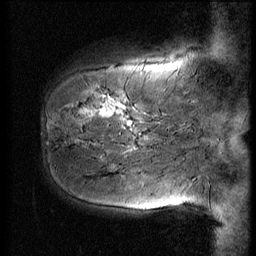
Breast MRI (dynamic contrast-enhanced), one sagittal slice. 3 images stored at this slice position (order not interpretable as contrast timing). 1.5 T. TE 4.2 ms, TR 9 ms. 2.5 mm slice thickness. 256 × 256 image matrix, field of view 180 × 180 mm. Female patient, age 51 years. Case-level facts recorded for this patient, not image findings: setting: breast cancer imaged before/during neoadjuvant chemotherapy; receptor status: HR-positive, HER2-negative.
Structures marked on this image (semi-automatic segmentation, software-assisted and operator-edited):
- analysis volume of interest (the breast-tissue region the enhancement analysis was run in; not a lesion): bounding box (x1, y1, x2, y2) in pixels: (41, 58, 167, 161)
- tumour enhancement mask (voxels above the 140 % enhancement threshold inside the analysis volume of interest): (81, 103, 133, 126)